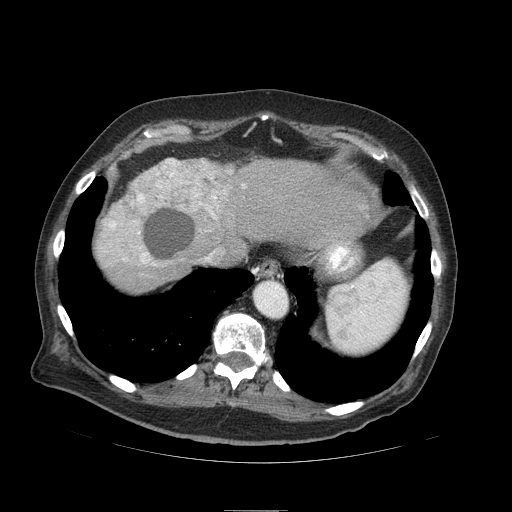
Contrast-enhanced abdominal CT (liver protocol), one axial slice. Slice 77 of 103 in the series (ordered by position). 120 kVp. Soft-tissue window (W 400 / L 40 HU). 2.5 mm slice thickness. 512 × 512 image matrix, field of view 440 × 440 mm. Case-level facts recorded for this patient, not image findings: diagnosis: hepatocellular carcinoma (patient treated with transarterial chemoembolisation; whether this scan precedes or follows treatment is not stated here); TNM stage (as recorded): Stage-IIIA; Child-Pugh class: B; tumour differentiation: well differentiated; tumour nodularity: multinodular.
Structures marked on this image (semi-automatic segmentation, software-assisted and operator-edited):
- liver parenchyma outside the tumour (the mass and vessels are separate outlines, so this box may not span the whole liver): bounding box <94,158,378,292> (left, top, right, bottom; pixels)
- mass: <97,156,243,266>